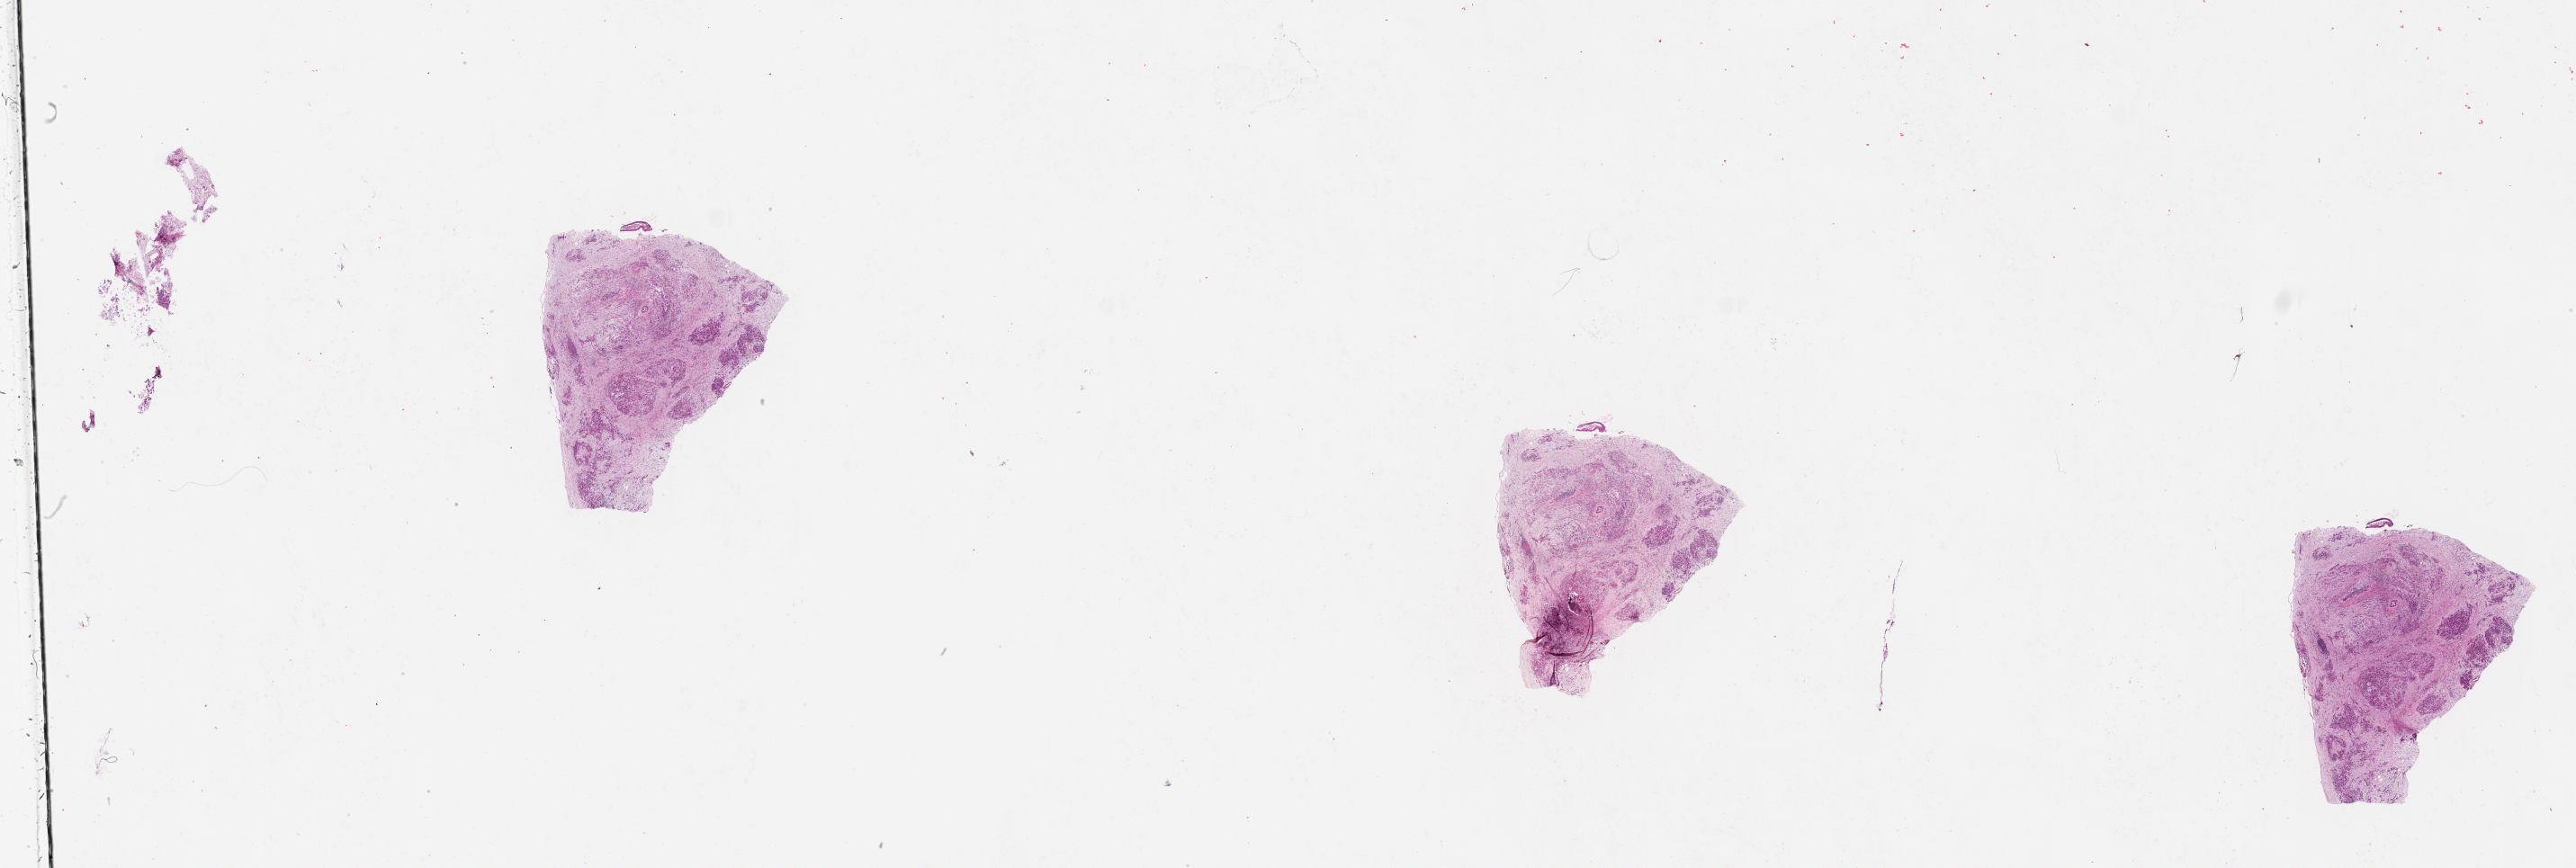
Digitized H&E tissue section (whole slide), whole scanned area (about 46.1 x 15.5 mm) shown as a low-resolution overview; tumour tissue sample, sampled site: pancreas. Patient: female, age 80 years. Histologic grade: G3 (poorly differentiated). Pathologist review of this section (percent, as recorded): tumour nuclei 50%, necrosis 0%.
* AJCC pathologic stage: III
* diagnosis: Infiltrating duct carcinoma, NOS
* primary tumour site (as recorded): head